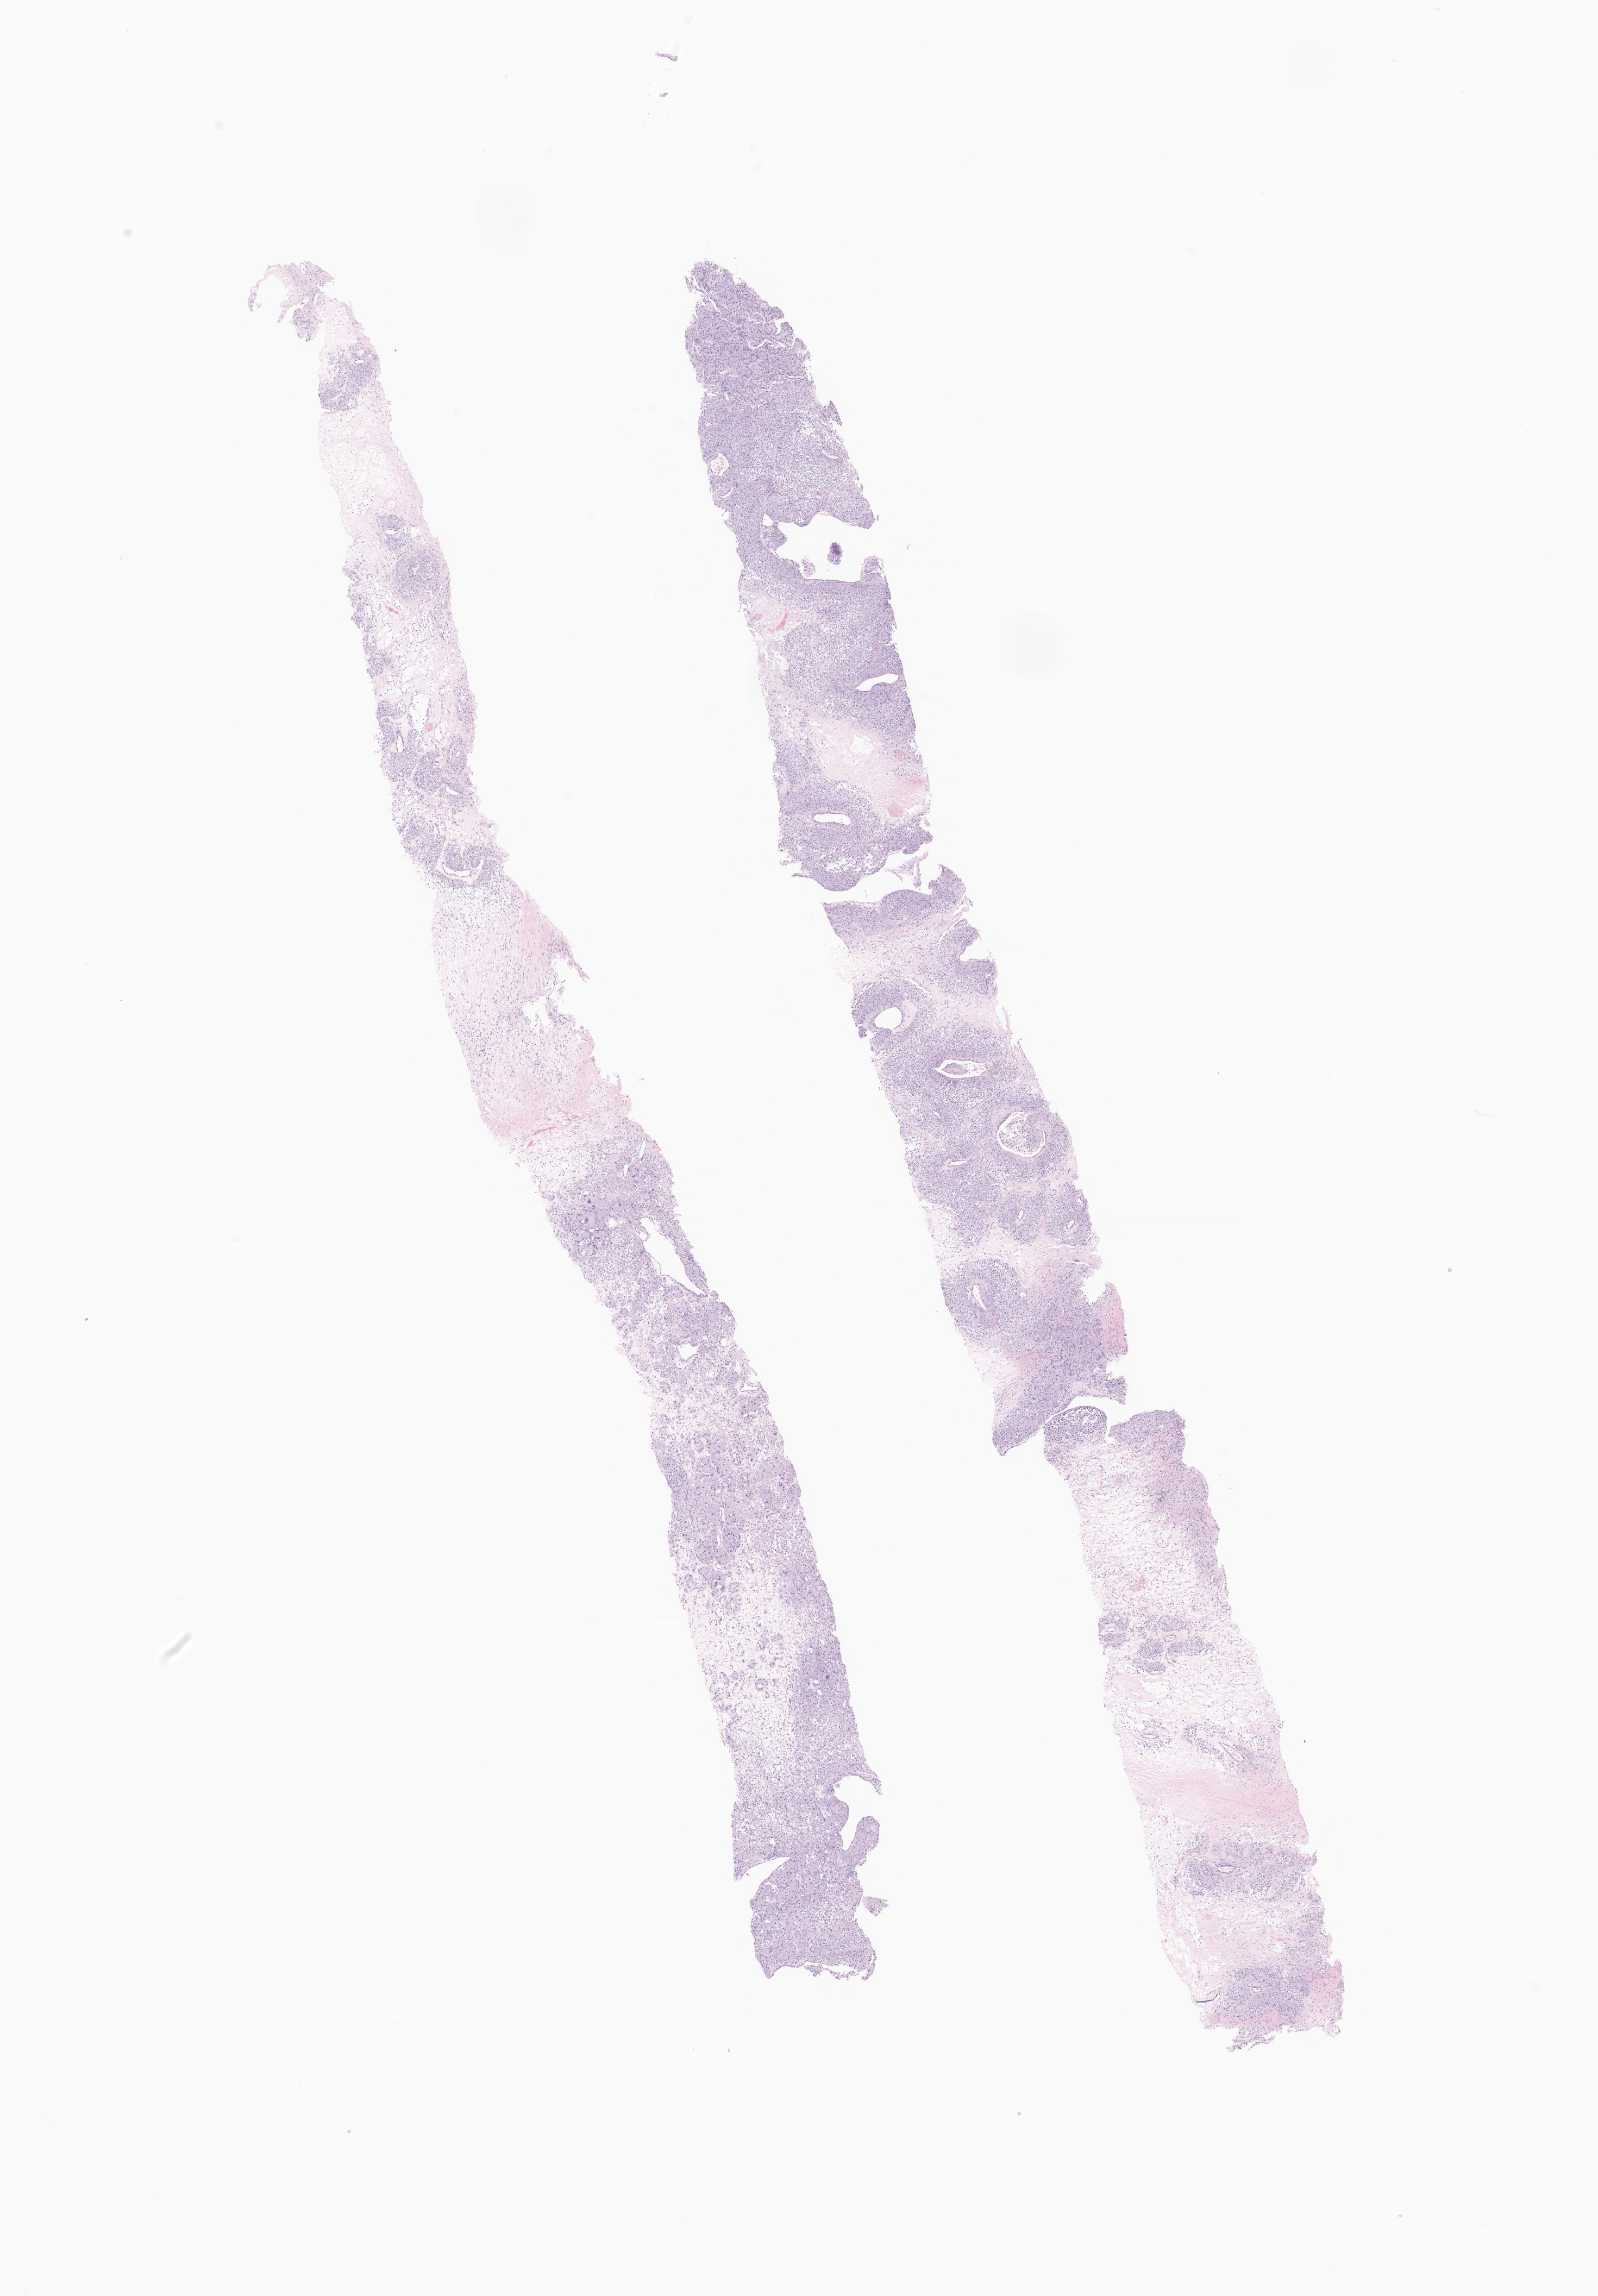
Digitized haematoxylin and eosin-stained section of tumor tissue from the long bone of lower limb, low-resolution overview of the scanned area, about 12.4 x 17.8 mm. Formalin-fixed paraffin-embedded section. Patient: male, age 271 months (22 years 7 months).
Diagnosis (ICD-O-3 morphology term): Alveolar soft part sarcoma.